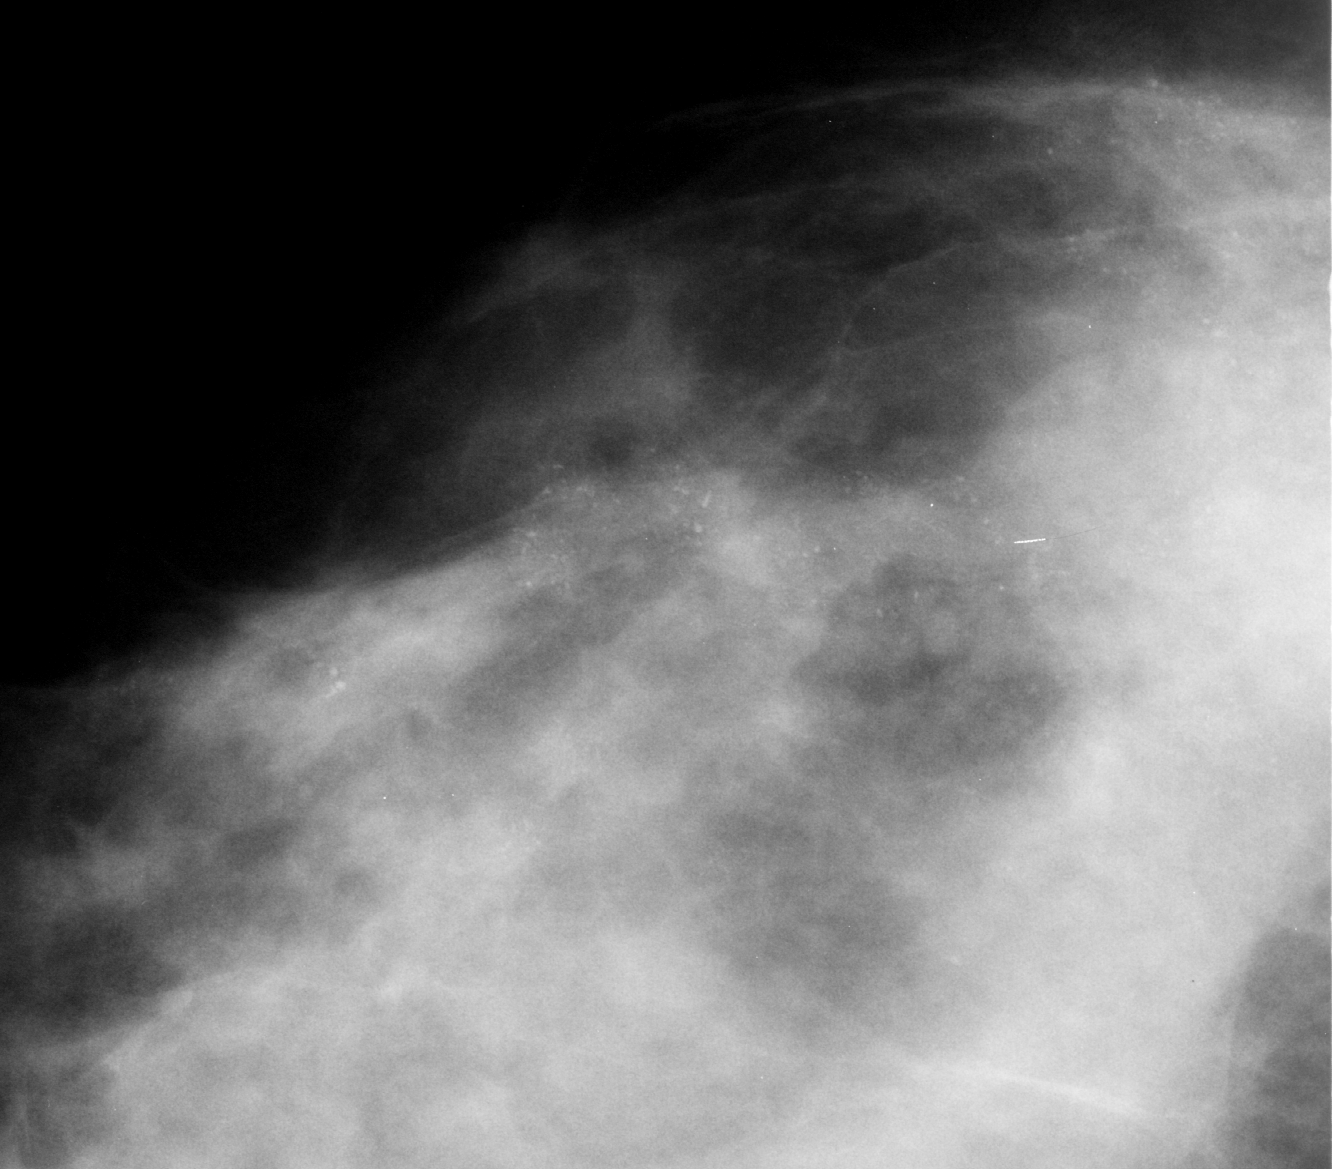
Cropped region of a digitized screen-film mammogram centred on a radiologist-marked abnormality; right breast; CC view.
Calcifications, morphology pleomorphic, distribution regional; BI-RADS assessment category 5; pathology (as recorded): malignant.